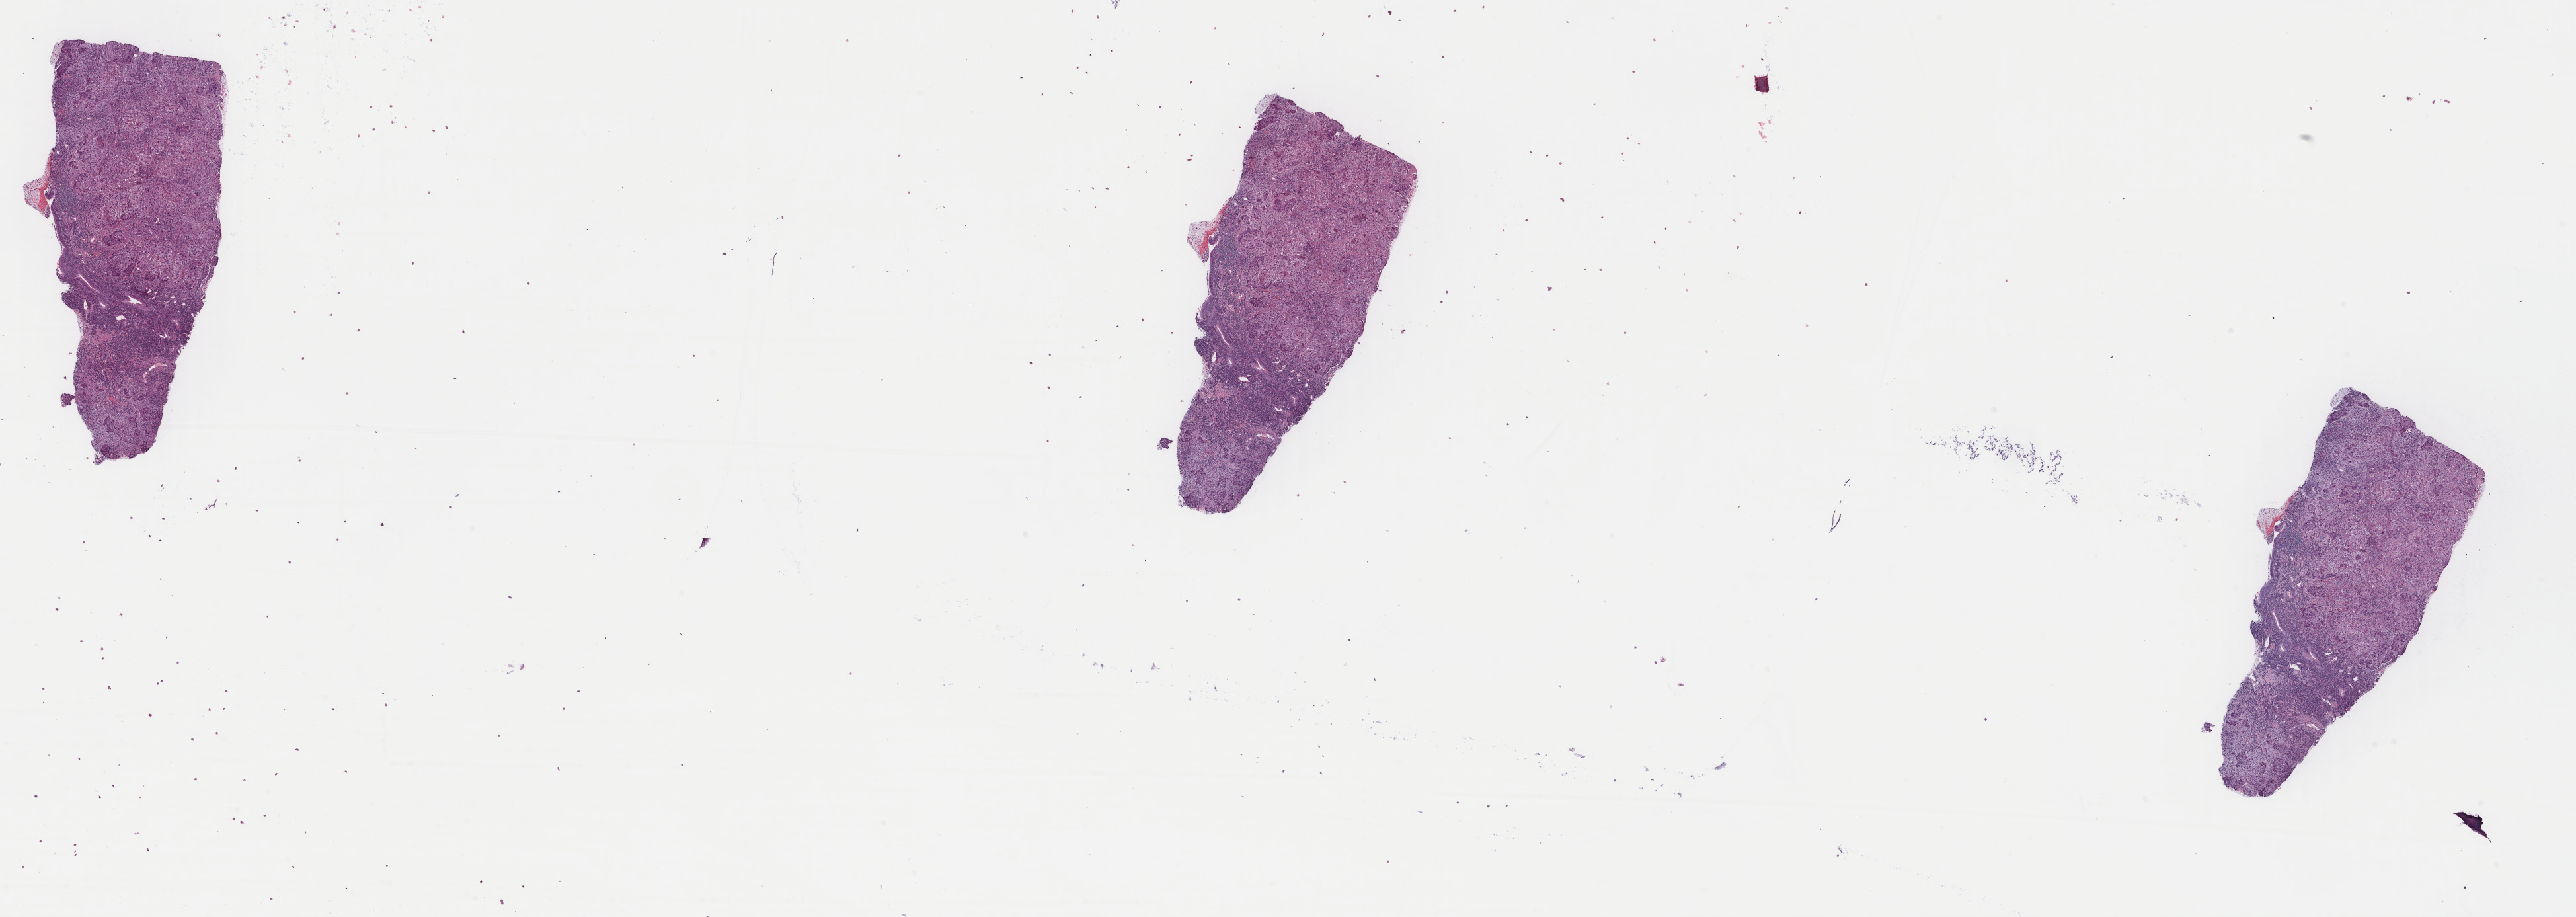
Hematoxylin and eosin (H&E) stained whole-slide image — low-resolution overview of the scanned area, about 30.9 x 11.0 mm, formalin-fixed paraffin-embedded (FFPE) diagnostic section, lung, primary tumour sample. Female, age 76 years at initial diagnosis.
Diagnosis: Squamous cell carcinoma, NOS.